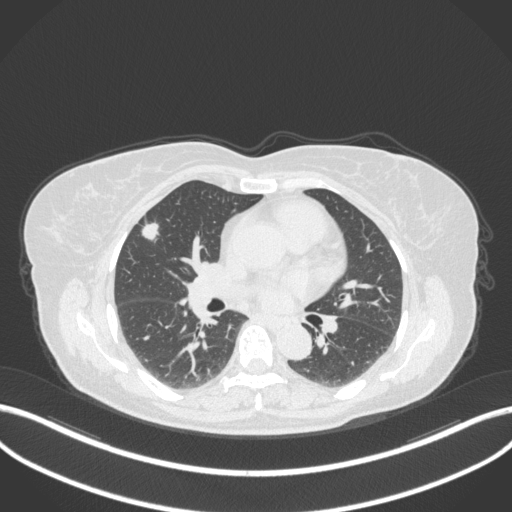
Chest CT, one axial slice. Position 178 of 310 along the scan axis. Reconstruction kernel B31f. Lung window (W 1500 / L -600 HU). 1 mm slice thickness. 512 × 512 image matrix, field of view 400 × 400 mm. Female patient, age 55 years. From the clinical record (not read from this slice): clinical TNM (as recorded): T1b N0 M0.
Outlined on this slice (rectangle marked by the reading radiologist):
- lung tumour (recorded histology: adenocarcinoma): bounding box <138,218,161,245> (left, top, right, bottom; pixels)